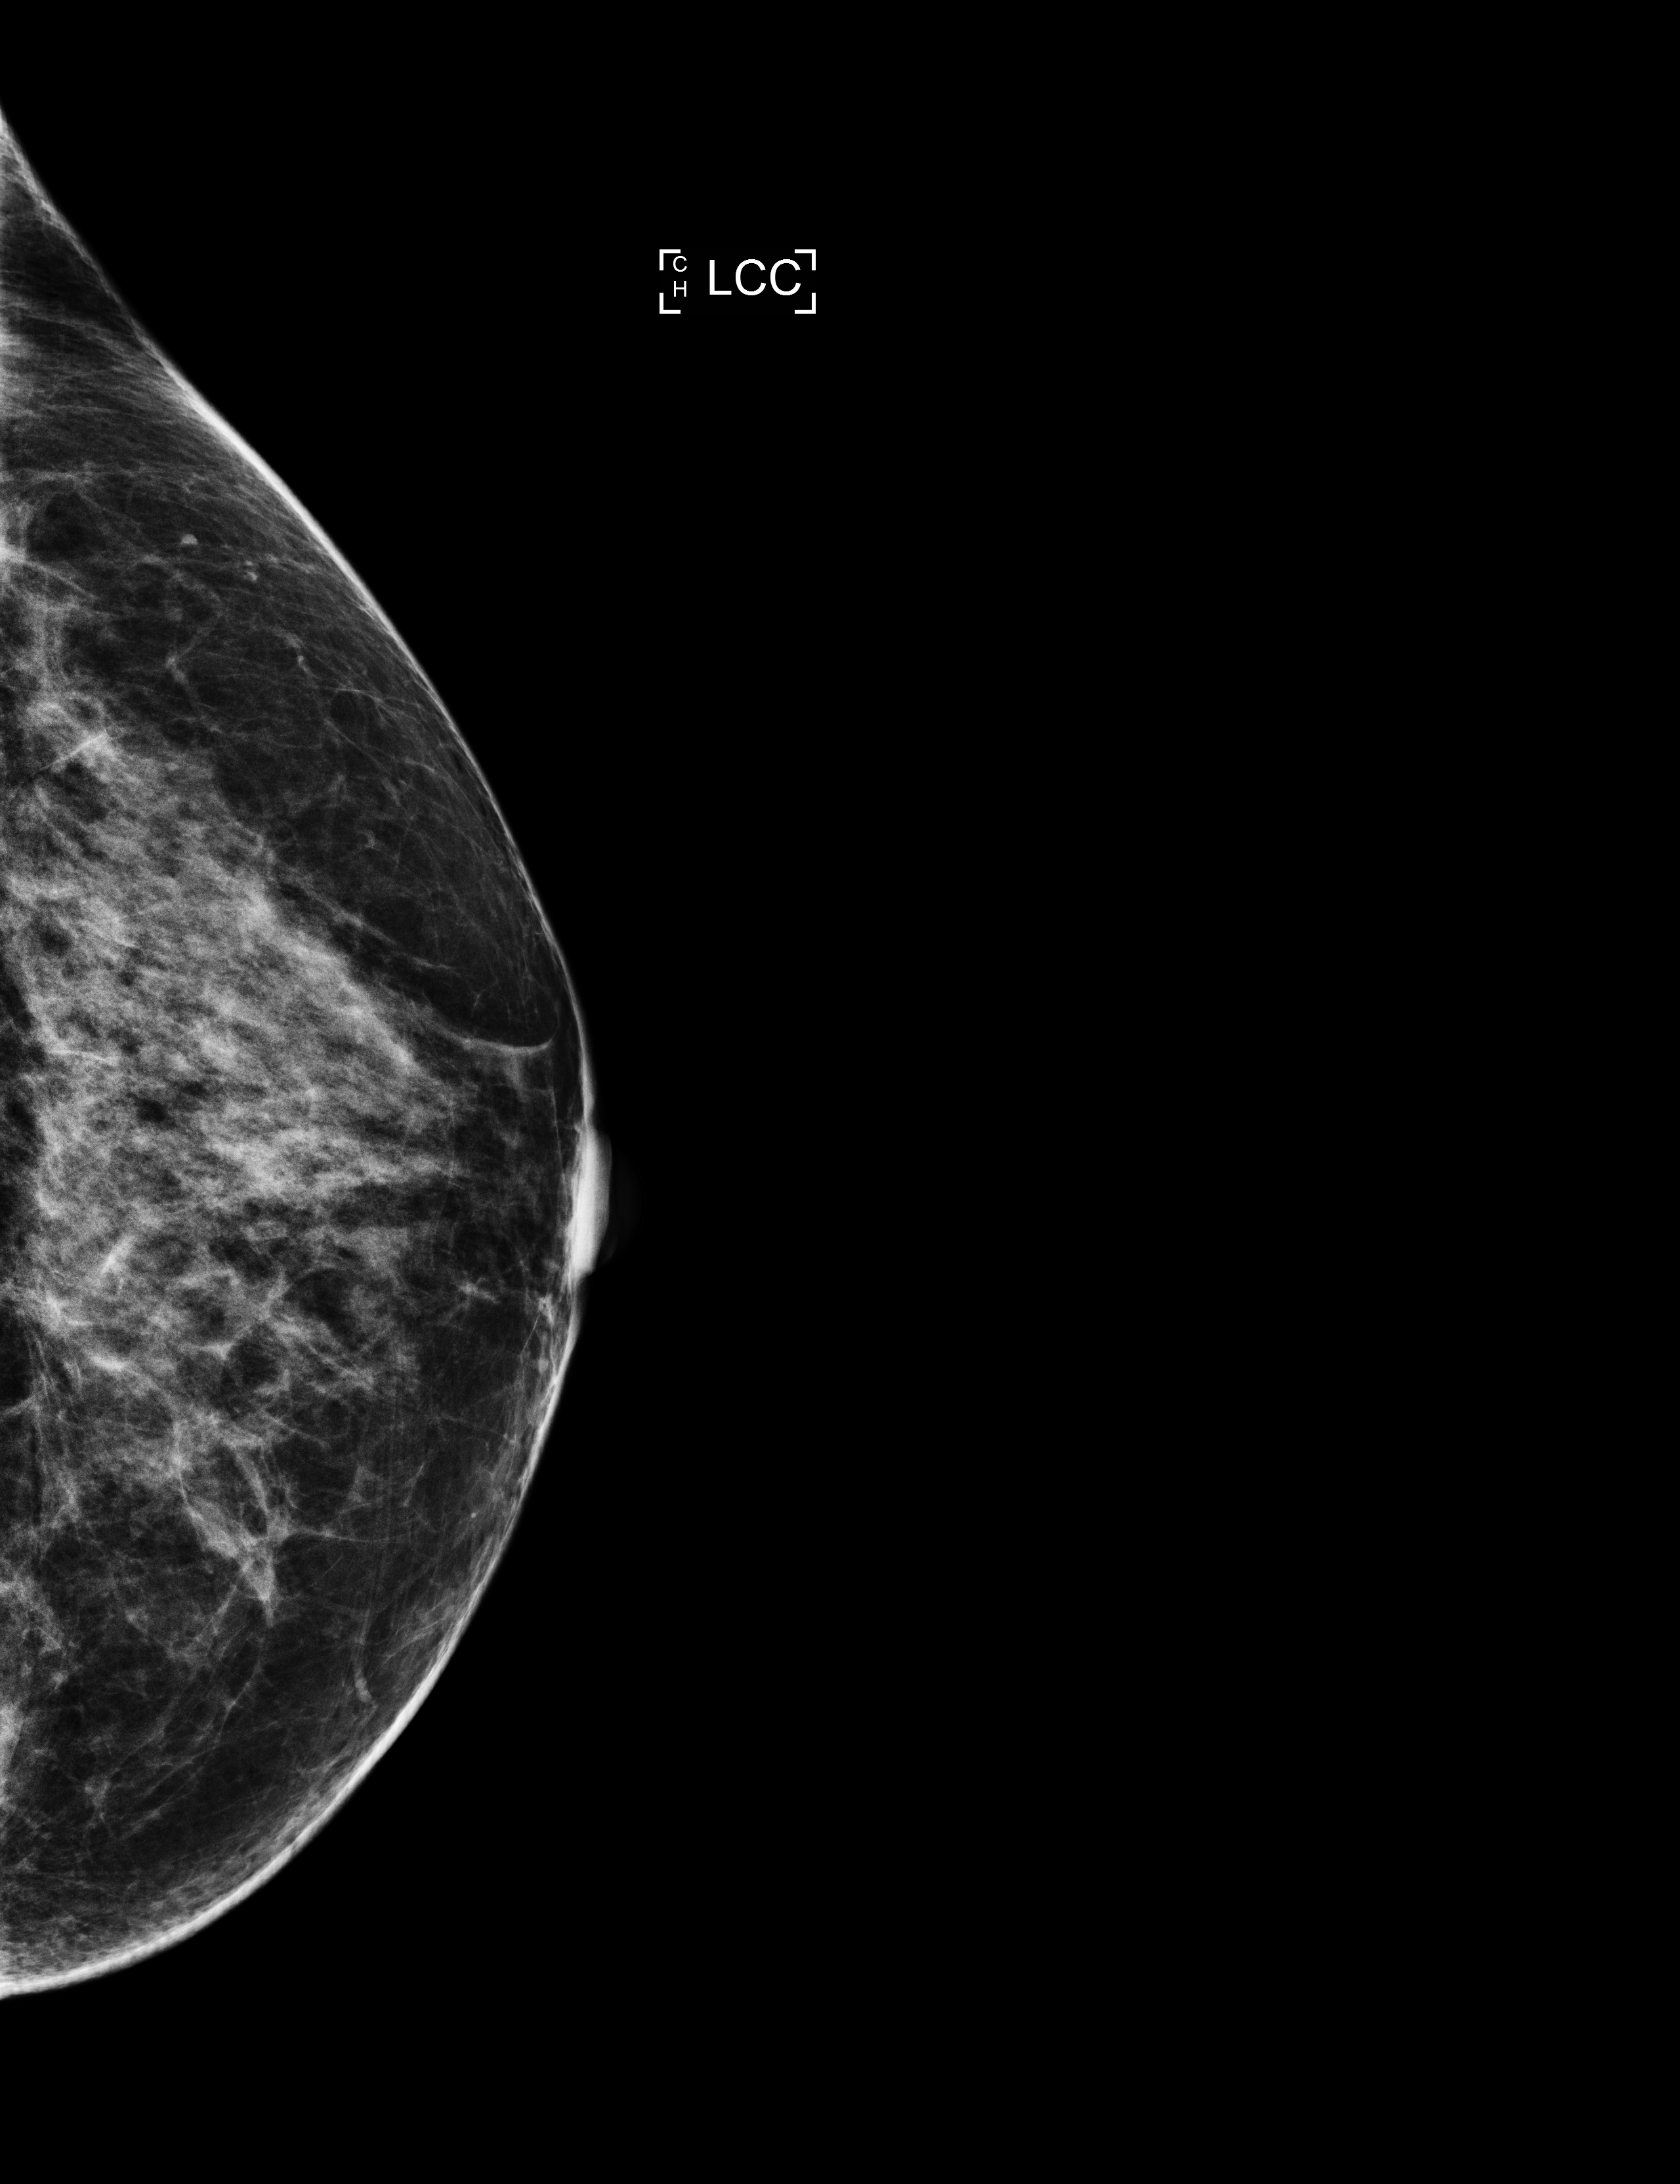
Annual screening mammography examination, system: Selenia Dimensions. Female patient, age 60 years.
Image type: full-field digital mammogram. Breast: left. Projection: CC view.